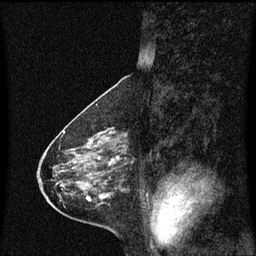
Breast MRI (dynamic contrast-enhanced), one sagittal slice; position 29 of 60 along the scan axis; dynamic contrast-enhanced series, image 2 of 3 at this slice position (ordered by acquisition); 1.5 T; TE 4.2 ms, TR 8.4 ms; 2 mm slice thickness; 256 × 256 image matrix, field of view 200 × 200 mm. Patient: female, 58 years.
Structures marked on this image (semi-automatically segmented with operator editing):
- analysis volume of interest (the breast-tissue region the enhancement analysis was run in; not a lesion): bounding box (x1, y1, x2, y2) in pixels: (100, 128, 129, 160)
- tumour enhancement mask (voxels above the 70 % enhancement threshold inside the analysis volume of interest): (100, 128, 119, 160)